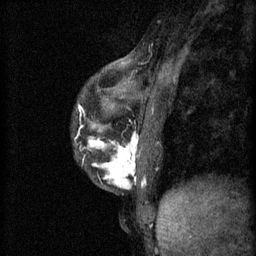
Breast MRI (dynamic contrast-enhanced), one sagittal slice. 3 images stored at this slice position (order not interpretable as contrast timing). 1.5 T. TE 4.2 ms, TR 11 ms. 256 × 256 image matrix. Patient: female, 37 years.
Outlined on this slice (semi-automatically segmented with operator editing):
- analysis volume of interest (the breast-tissue region the enhancement analysis was run in; not a lesion): bounding box (x1, y1, x2, y2) in pixels: (76, 120, 152, 191)
- tumour enhancement mask (voxels above the 70 % enhancement threshold inside the analysis volume of interest): (89, 132, 138, 189)